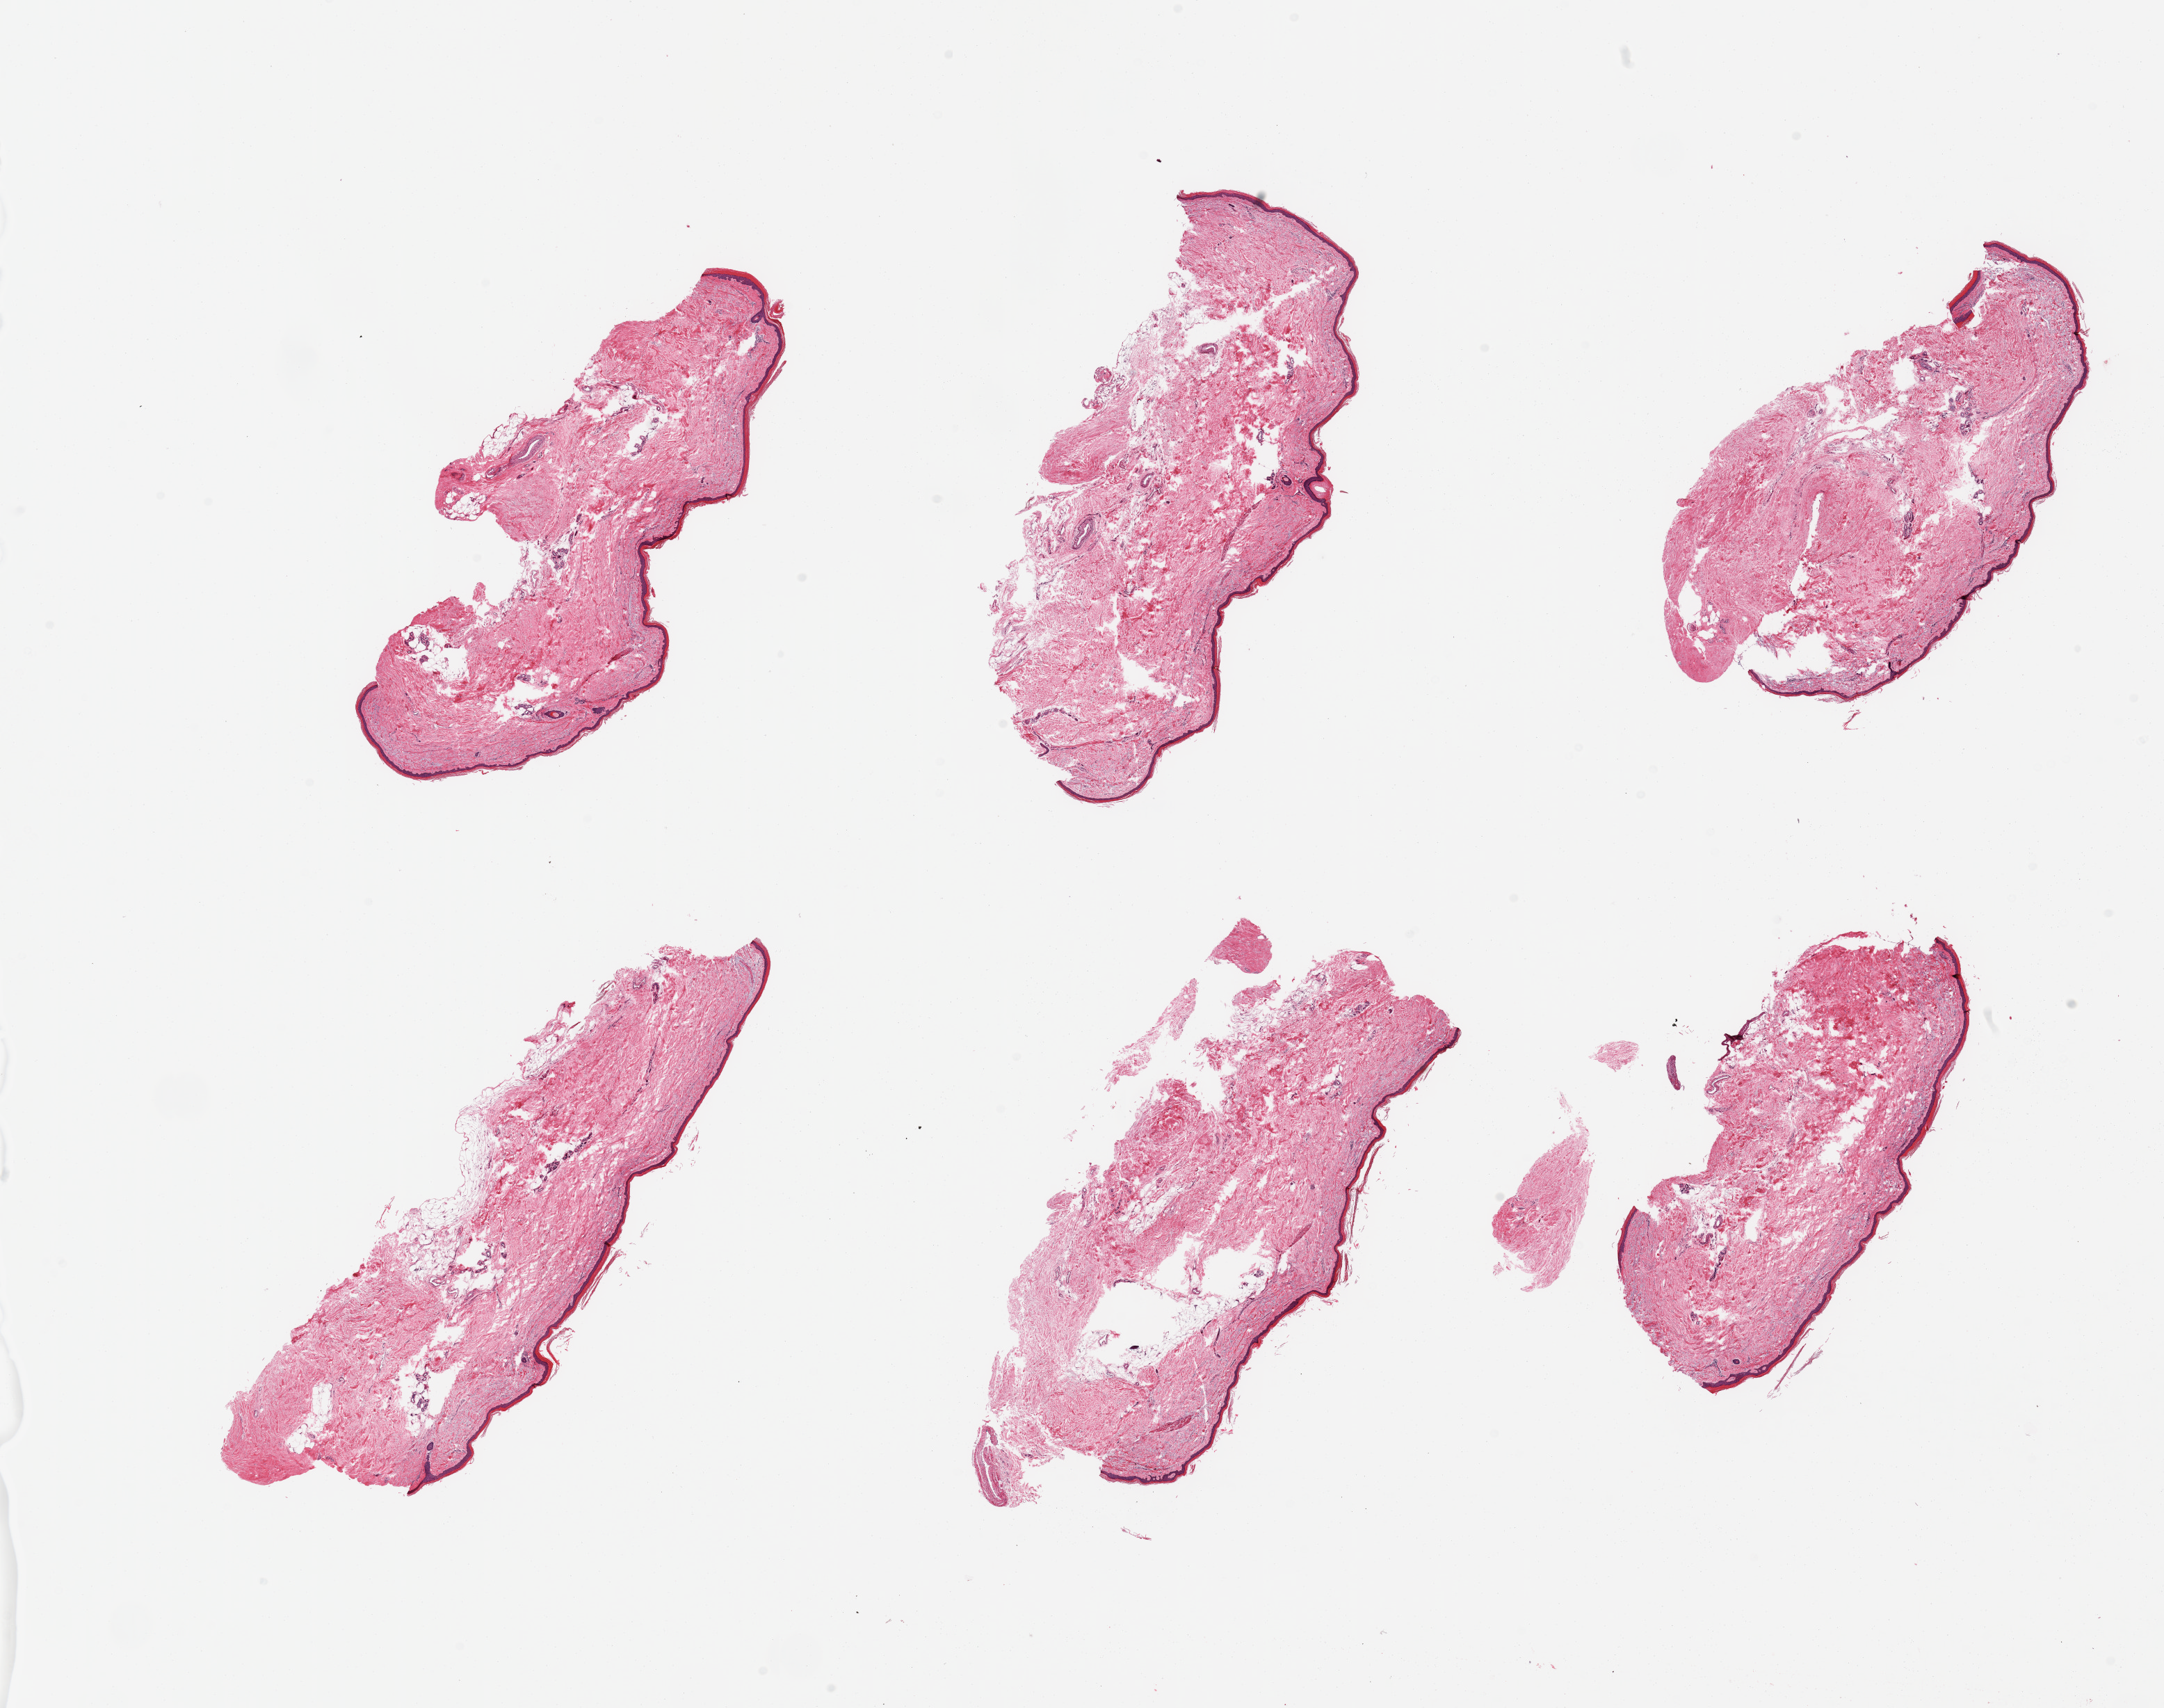
Hematoxylin and eosin (H&E) whole-slide image, brightfield — a low-resolution overview of the entire scanned area, about 24.6 x 19.4 mm (acquisition: 20x scan). PAXgene-fixed, paraffin-embedded tissue. Section of skin of lower leg (target tissue). Donor tissue sample. Donor: female.
Reviewer comment on this tissue sample: 6 pieces; ~10% - 15% internal/periadnexal fat; epidermis ~35 microns thick.